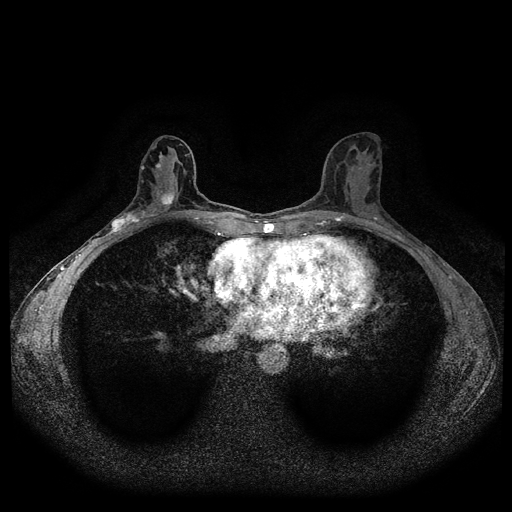
Breast MRI (dynamic contrast-enhanced, multi-phase), one axial slice. Slice 52 of 116 in the series (ordered by position). Dynamic contrast-enhanced series, time point 2 of 5 at this slice position (early post-contrast). 1.5 T. TE 2.6 ms, TR 5.3 ms. 2 mm slice thickness. 512 × 512 image matrix, field of view 350 × 350 mm. Female patient, age 50 years.
Structures marked on this image (semi-automatically segmented with operator editing):
- breast lesion (labelled 'tumour' in the annotation; benign lesions carry a separate 'benign' label): bounding box [x1, y1, x2, y2] px = [110, 190, 175, 235]